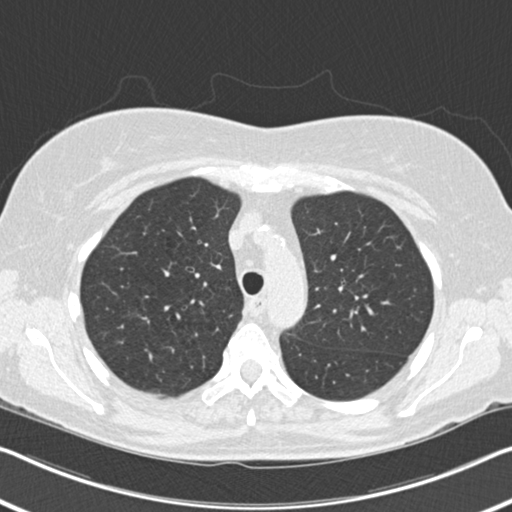
Low-dose screening chest CT, axial slice, second screening round (one year after baseline), lung window (W 1500 / L -600 HU), 120 kVp, slice 57 of 202 in the series, 512 × 512 image matrix, field of view 336 × 336 mm. Female, age 60 years at enrolment. Current smoker at enrolment.
Expert-annotated lung lesion, bounding box [x1, y1, x2, y2] px = [382, 230, 422, 266]. The screening reader recorded 6 non-calcified nodules or masses ≥4 mm on this exam; which of them this box marks is not recorded. Official screen result: positive, change unspecified: nodule(s) >= 4 mm or enlarging nodule(s), mass(es), or other non-specific abnormalities suspicious for lung cancer.